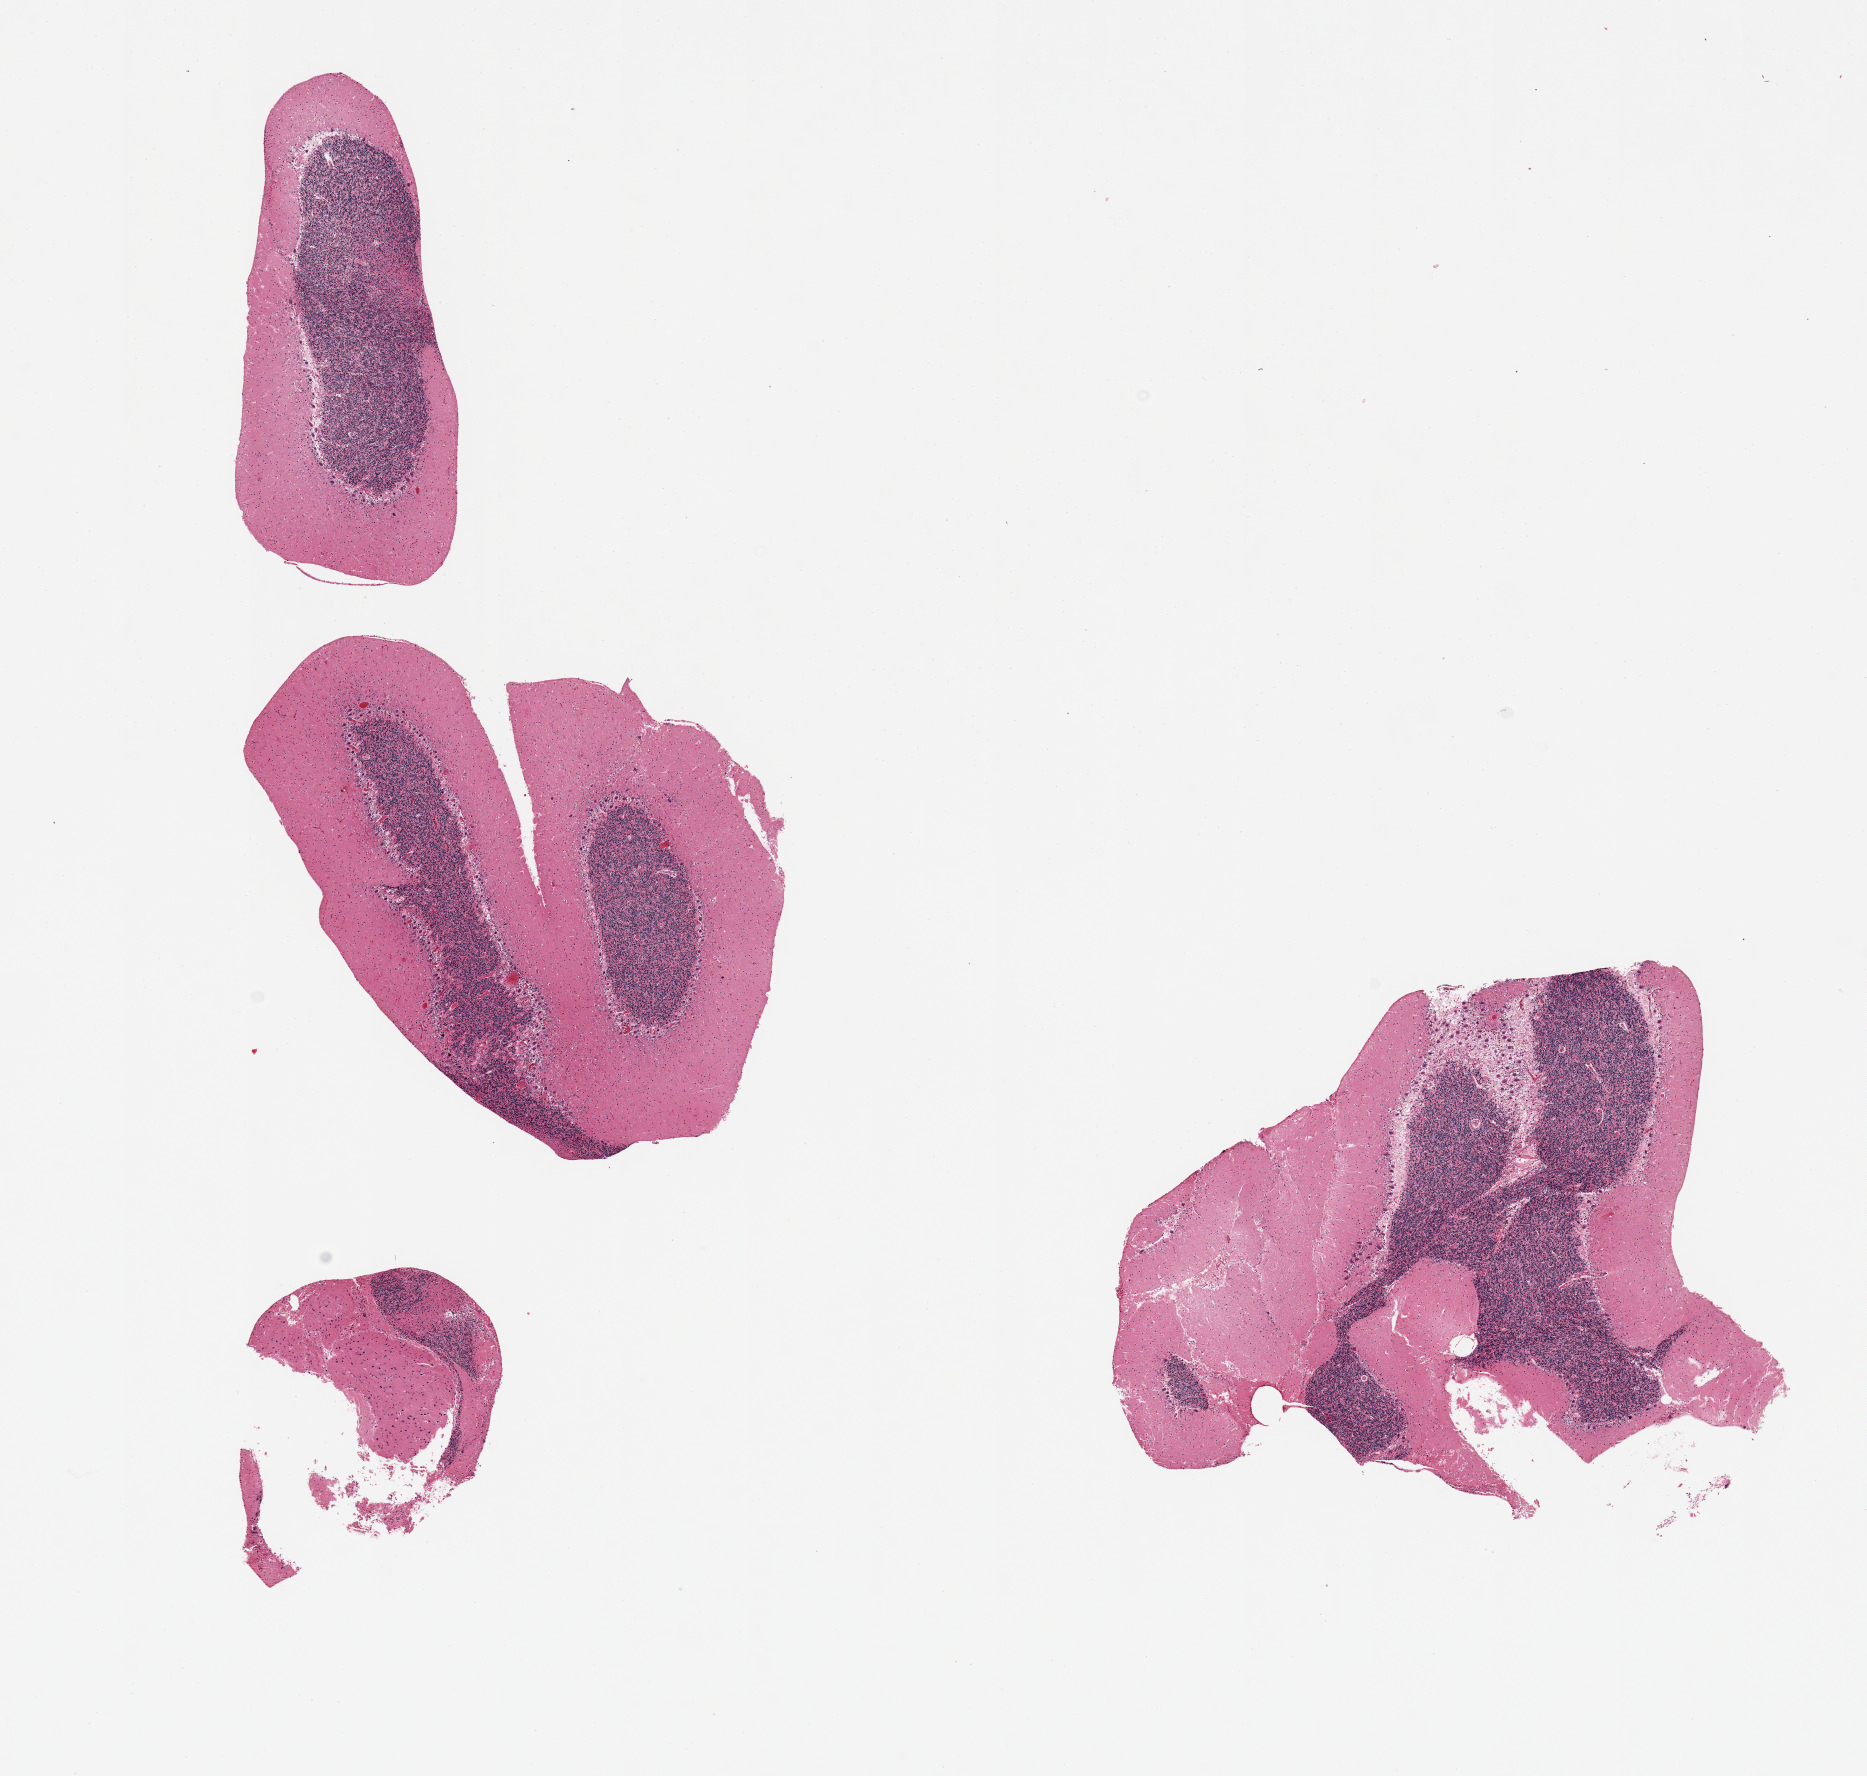
Whole-slide image, haematoxylin and eosin stain, brightfield, whole scanned area (about 14.8 x 14.0 mm, from a 20x scan) shown as a low-resolution overview; PAXgene-fixed, paraffin-embedded tissue; sampled site (target tissue): cerebellum; tissue donor sample. Donor sex: female.
Pathologist's review note for this sample: 4 pieces; CEREBELLUM NOT CORTEX (as originally labeled).